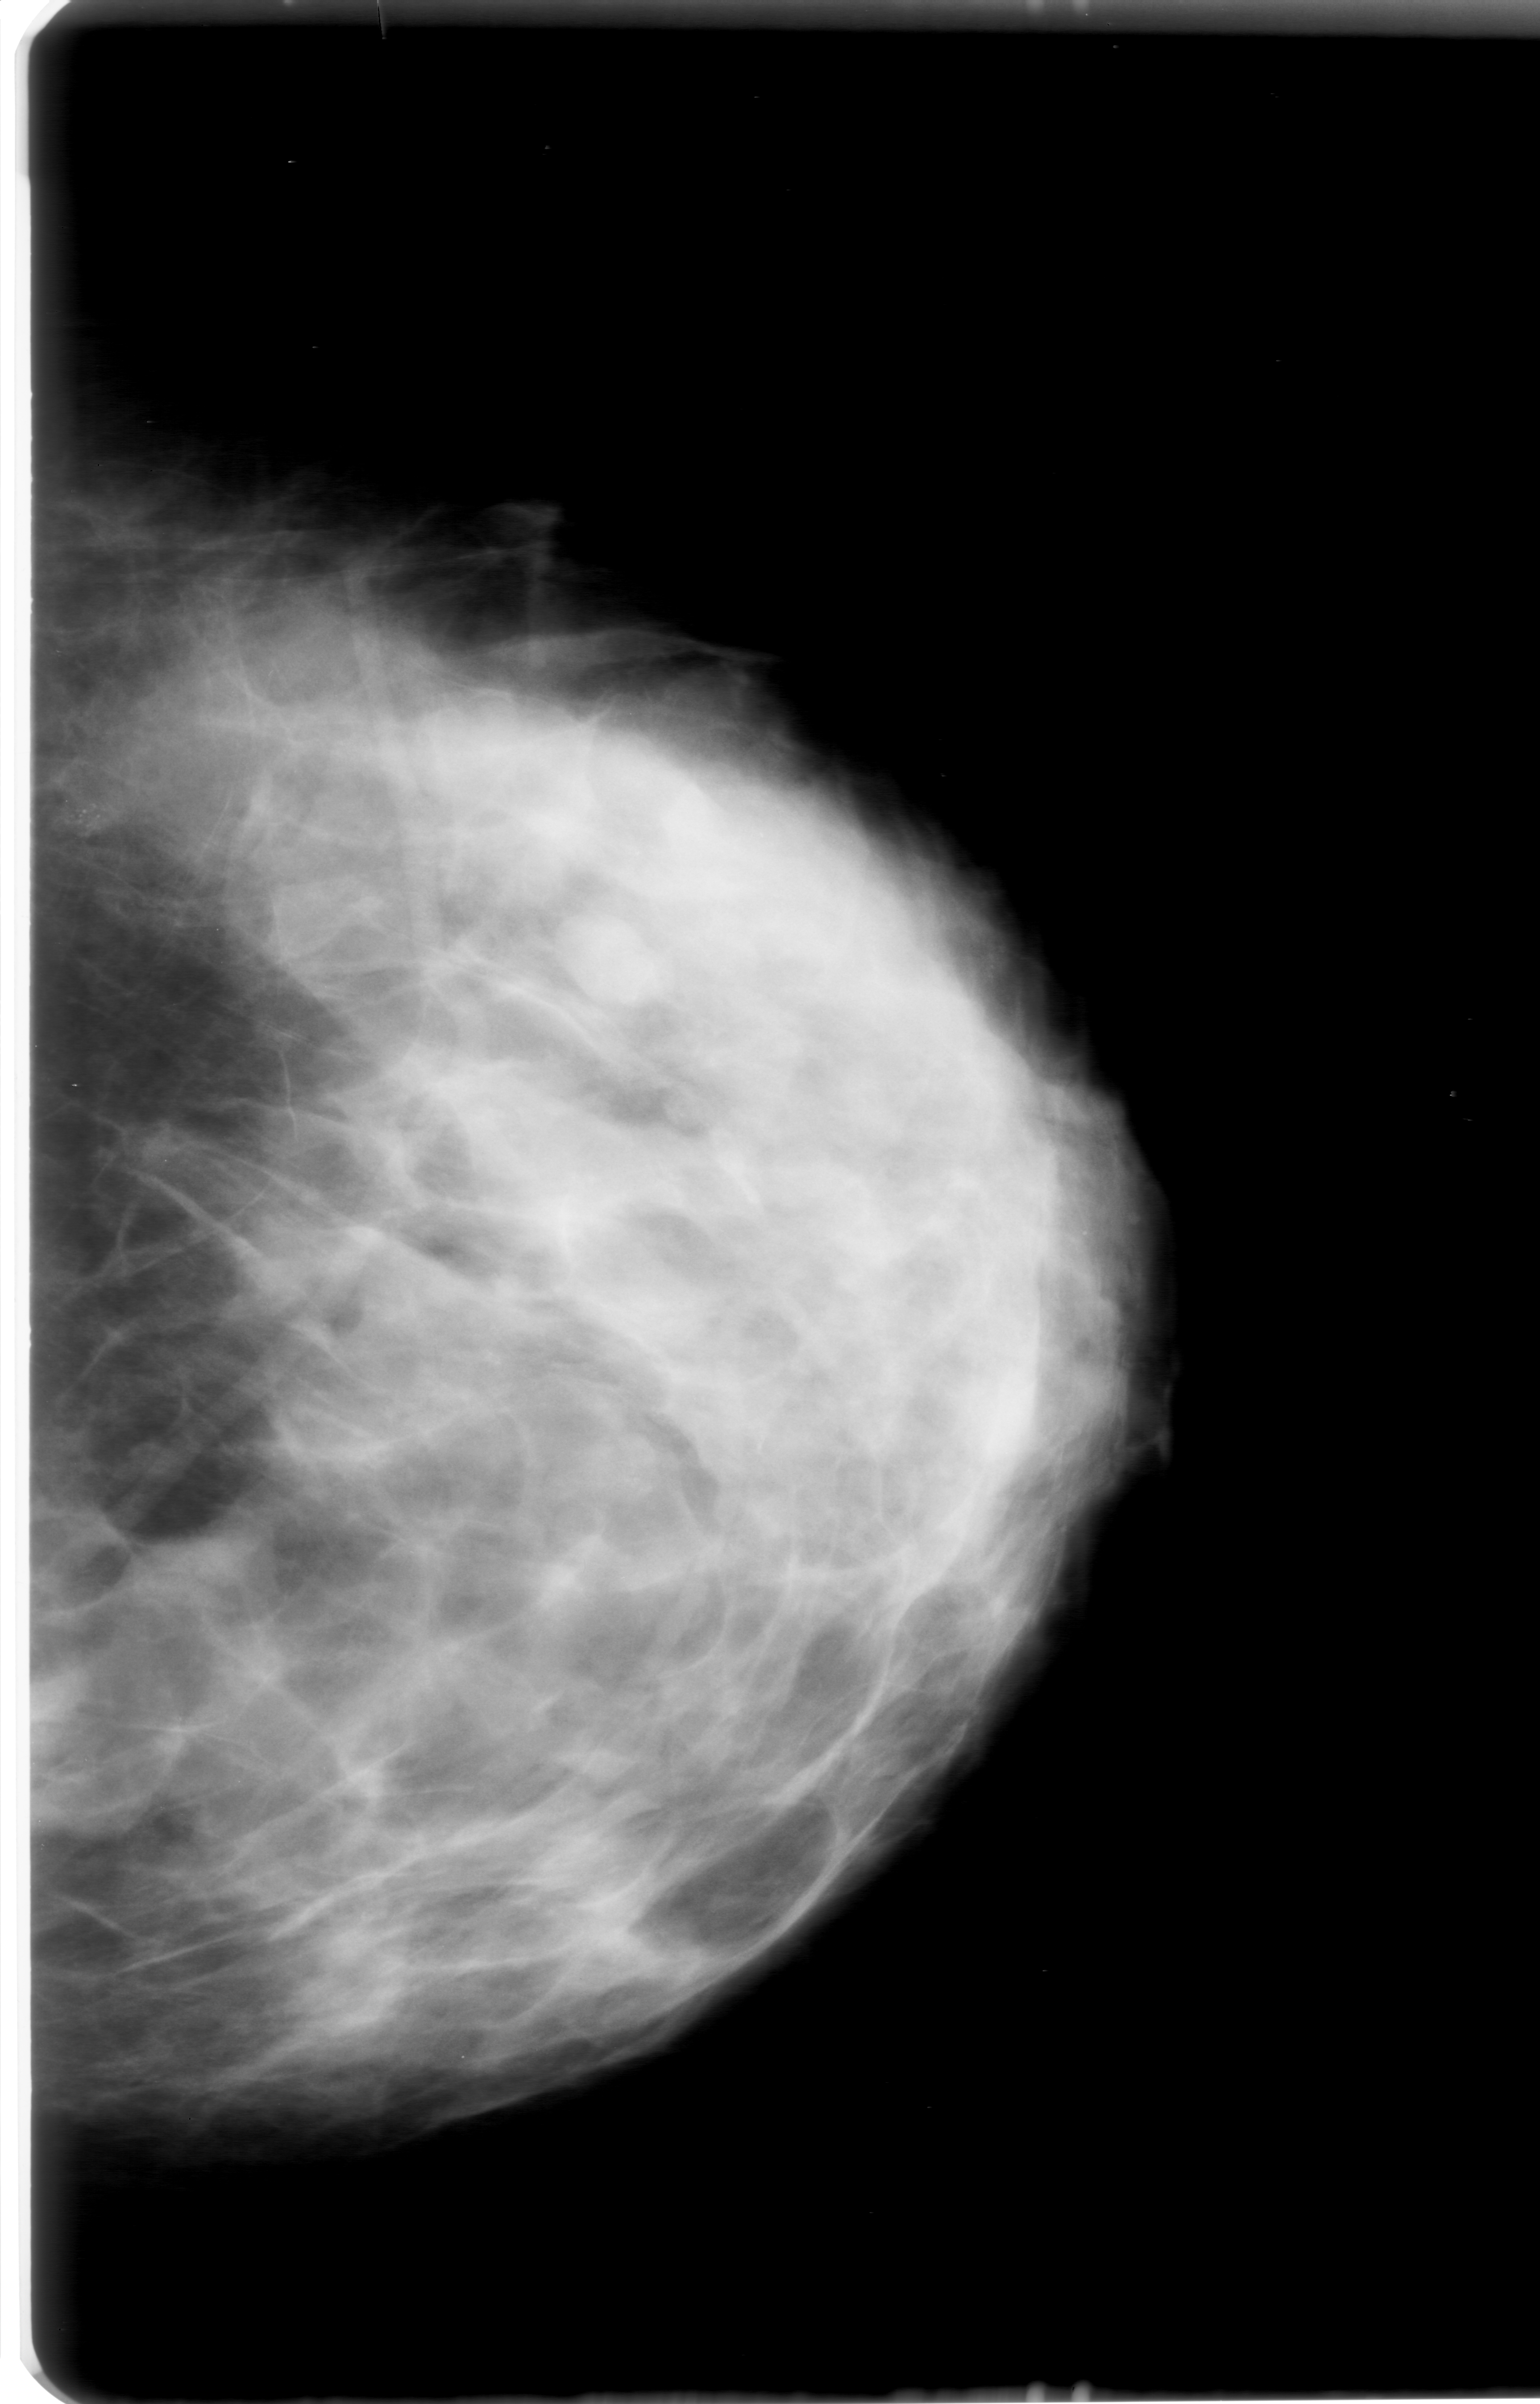
Digitized screen-film mammogram; left breast; craniocaudal (CC) view; breast composition: heterogeneously dense (BI-RADS density category 3 of 4).
Calcifications, morphology round and regular / pleomorphic, distribution clustered; BI-RADS assessment category 0; pathology result (as recorded, not read from the image): benign.